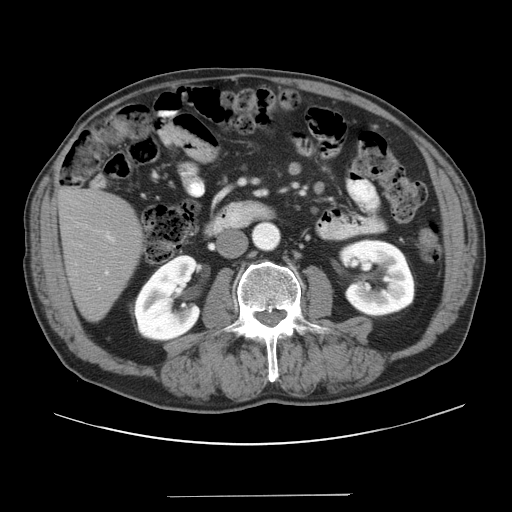
Contrast-enhanced abdominal CT, one axial slice; position 7 of 41 along the scan axis; 120 kVp; intravenous contrast given; soft-tissue window (W 400 / L 40 HU); 5 mm slice thickness; 512 × 512 image matrix. Male patient, age 75 years. Case-level facts recorded for this patient, not image findings: diagnosis: colorectal cancer liver metastases, imaged before liver resection; multiple liver metastases: no; largest metastasis: 5.2 cm; disease in both lobes: no.
Structures marked on this image (expert manual segmentation):
- liver: bounding box <60,192,142,317> (left, top, right, bottom; pixels)
- planned liver remnant (the part of the liver to remain after resection): <60,192,142,317>
- portal vein (with intrahepatic branches): <105,232,115,275>